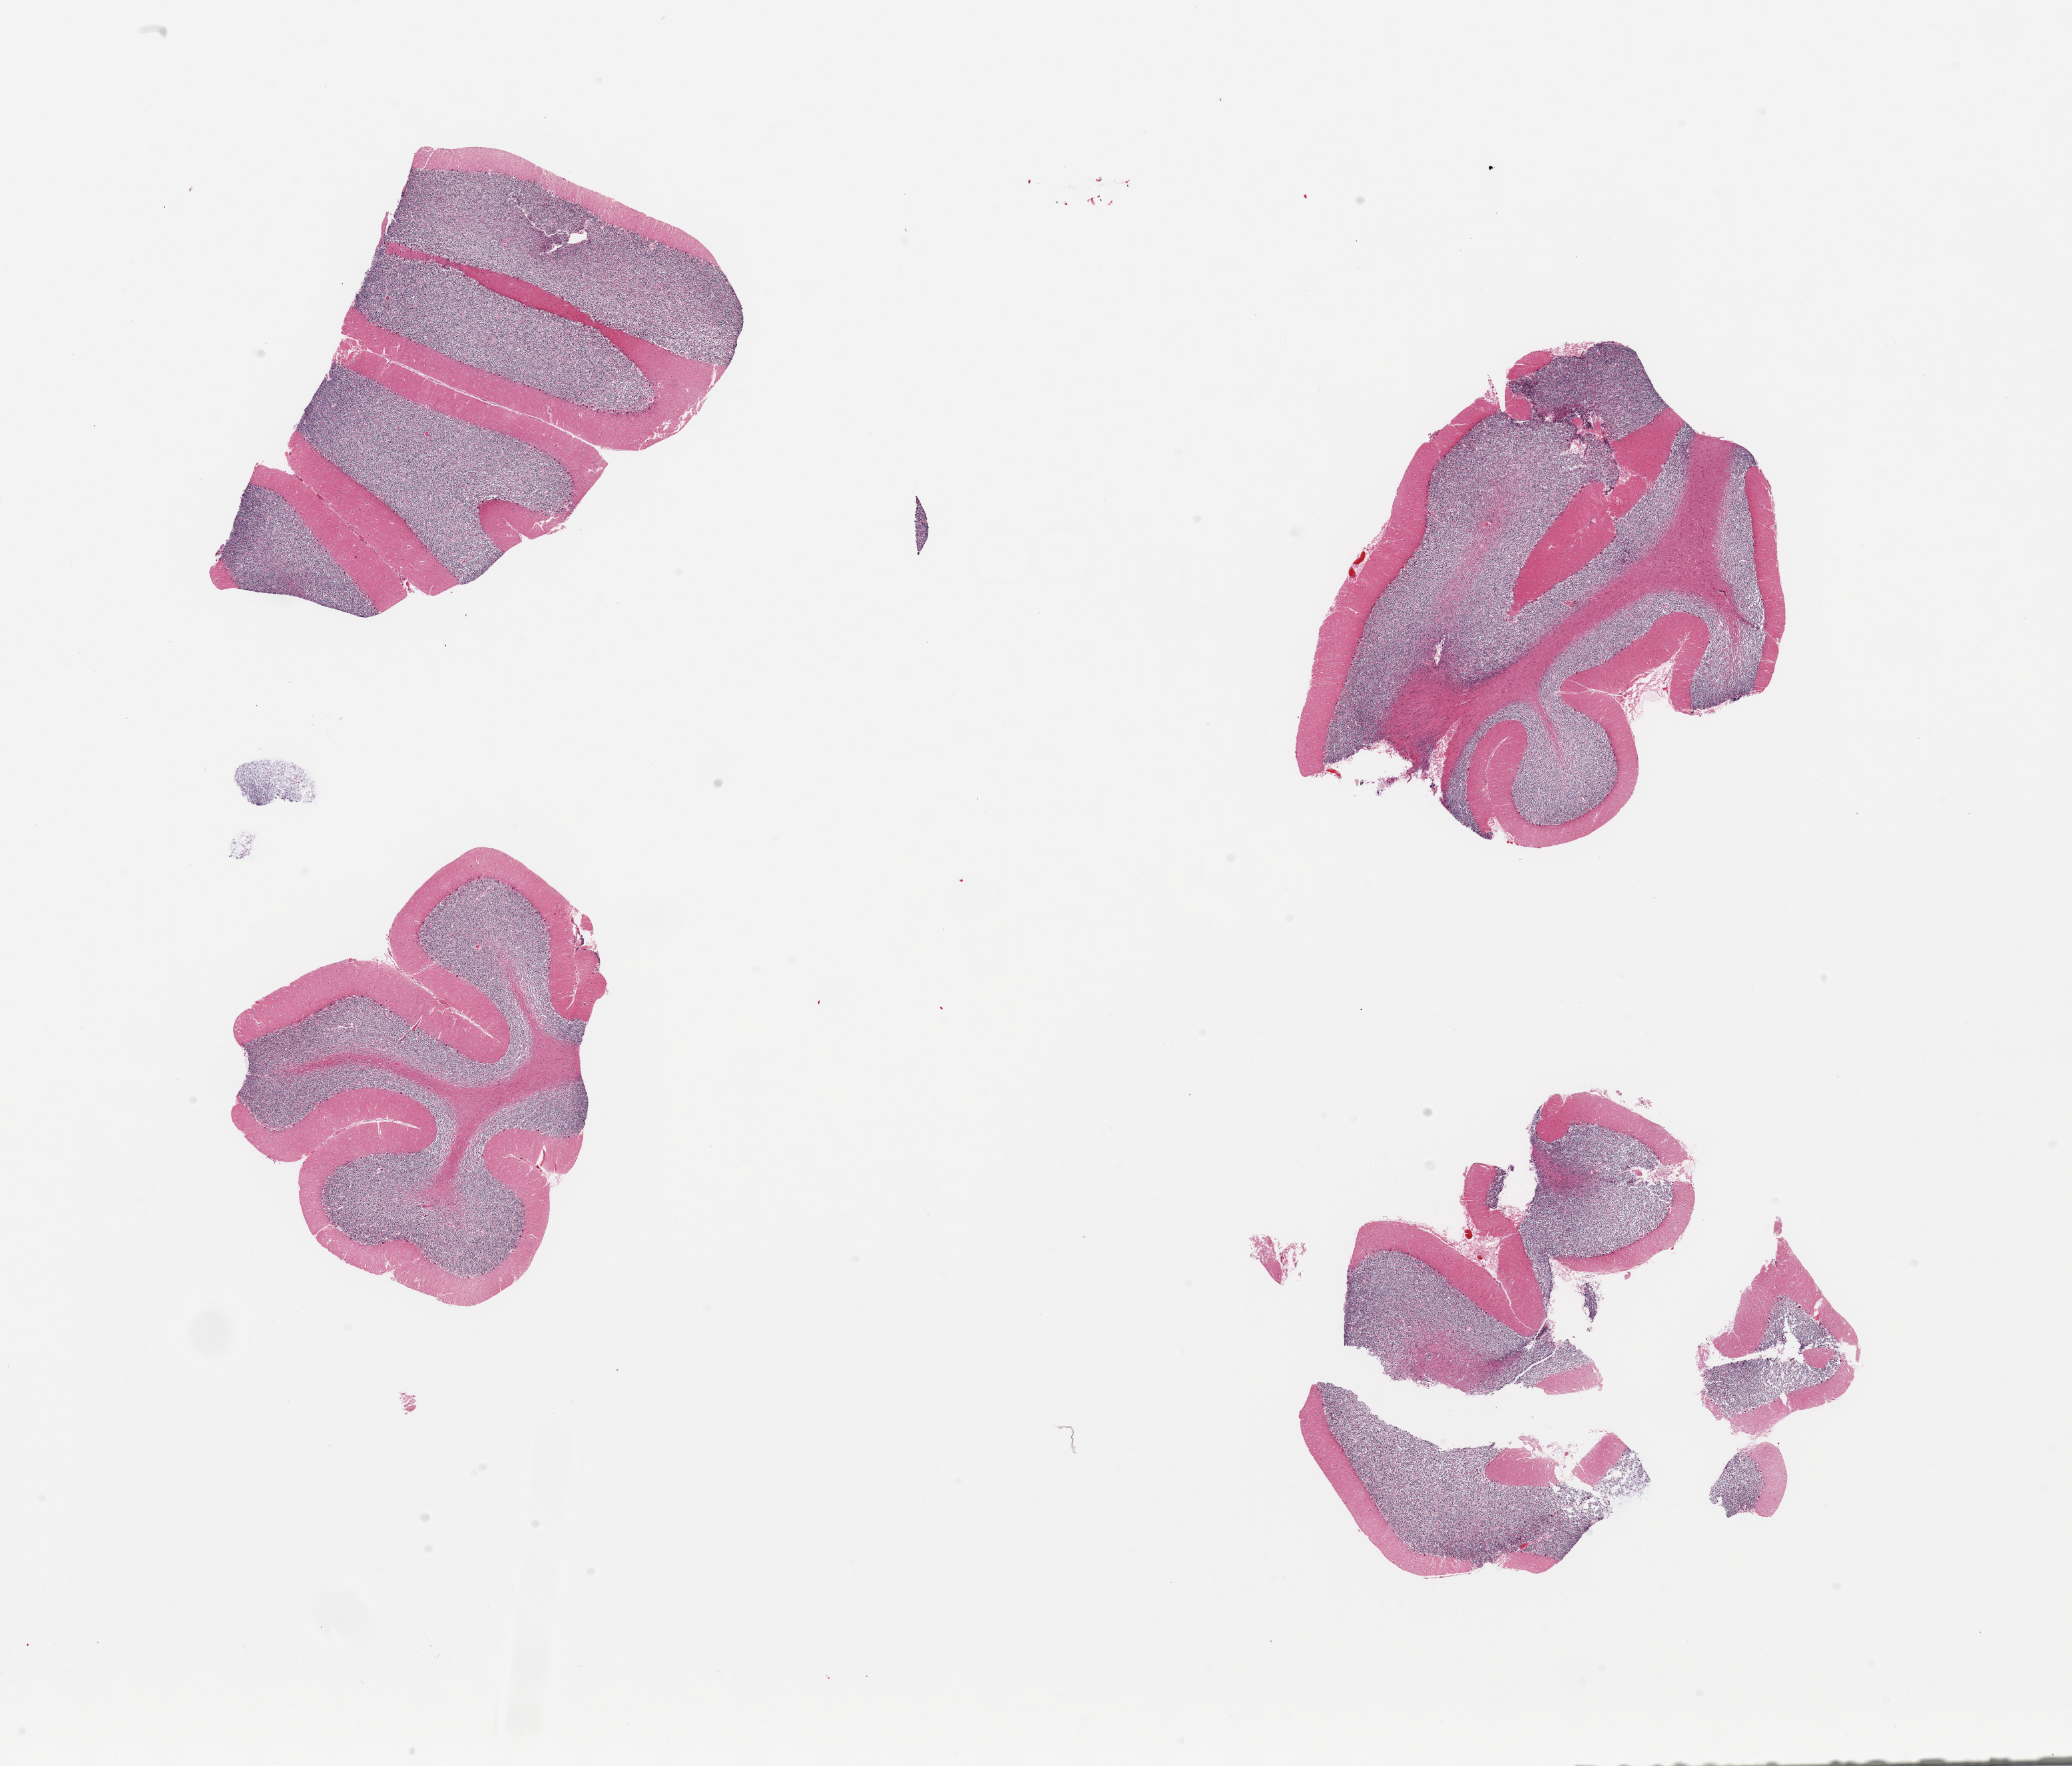
Whole-slide image, hematoxylin and eosin (H&E) stain, a low-resolution overview of the entire scanned area, about 24.6 x 21.0 mm (from a 20x scan), PAXgene-fixed, paraffin-embedded tissue, sampled site (target tissue): cerebellum, tissue donor sample. Donor sex: female.
Review note (as recorded): 4 pieces, no abnormalities.